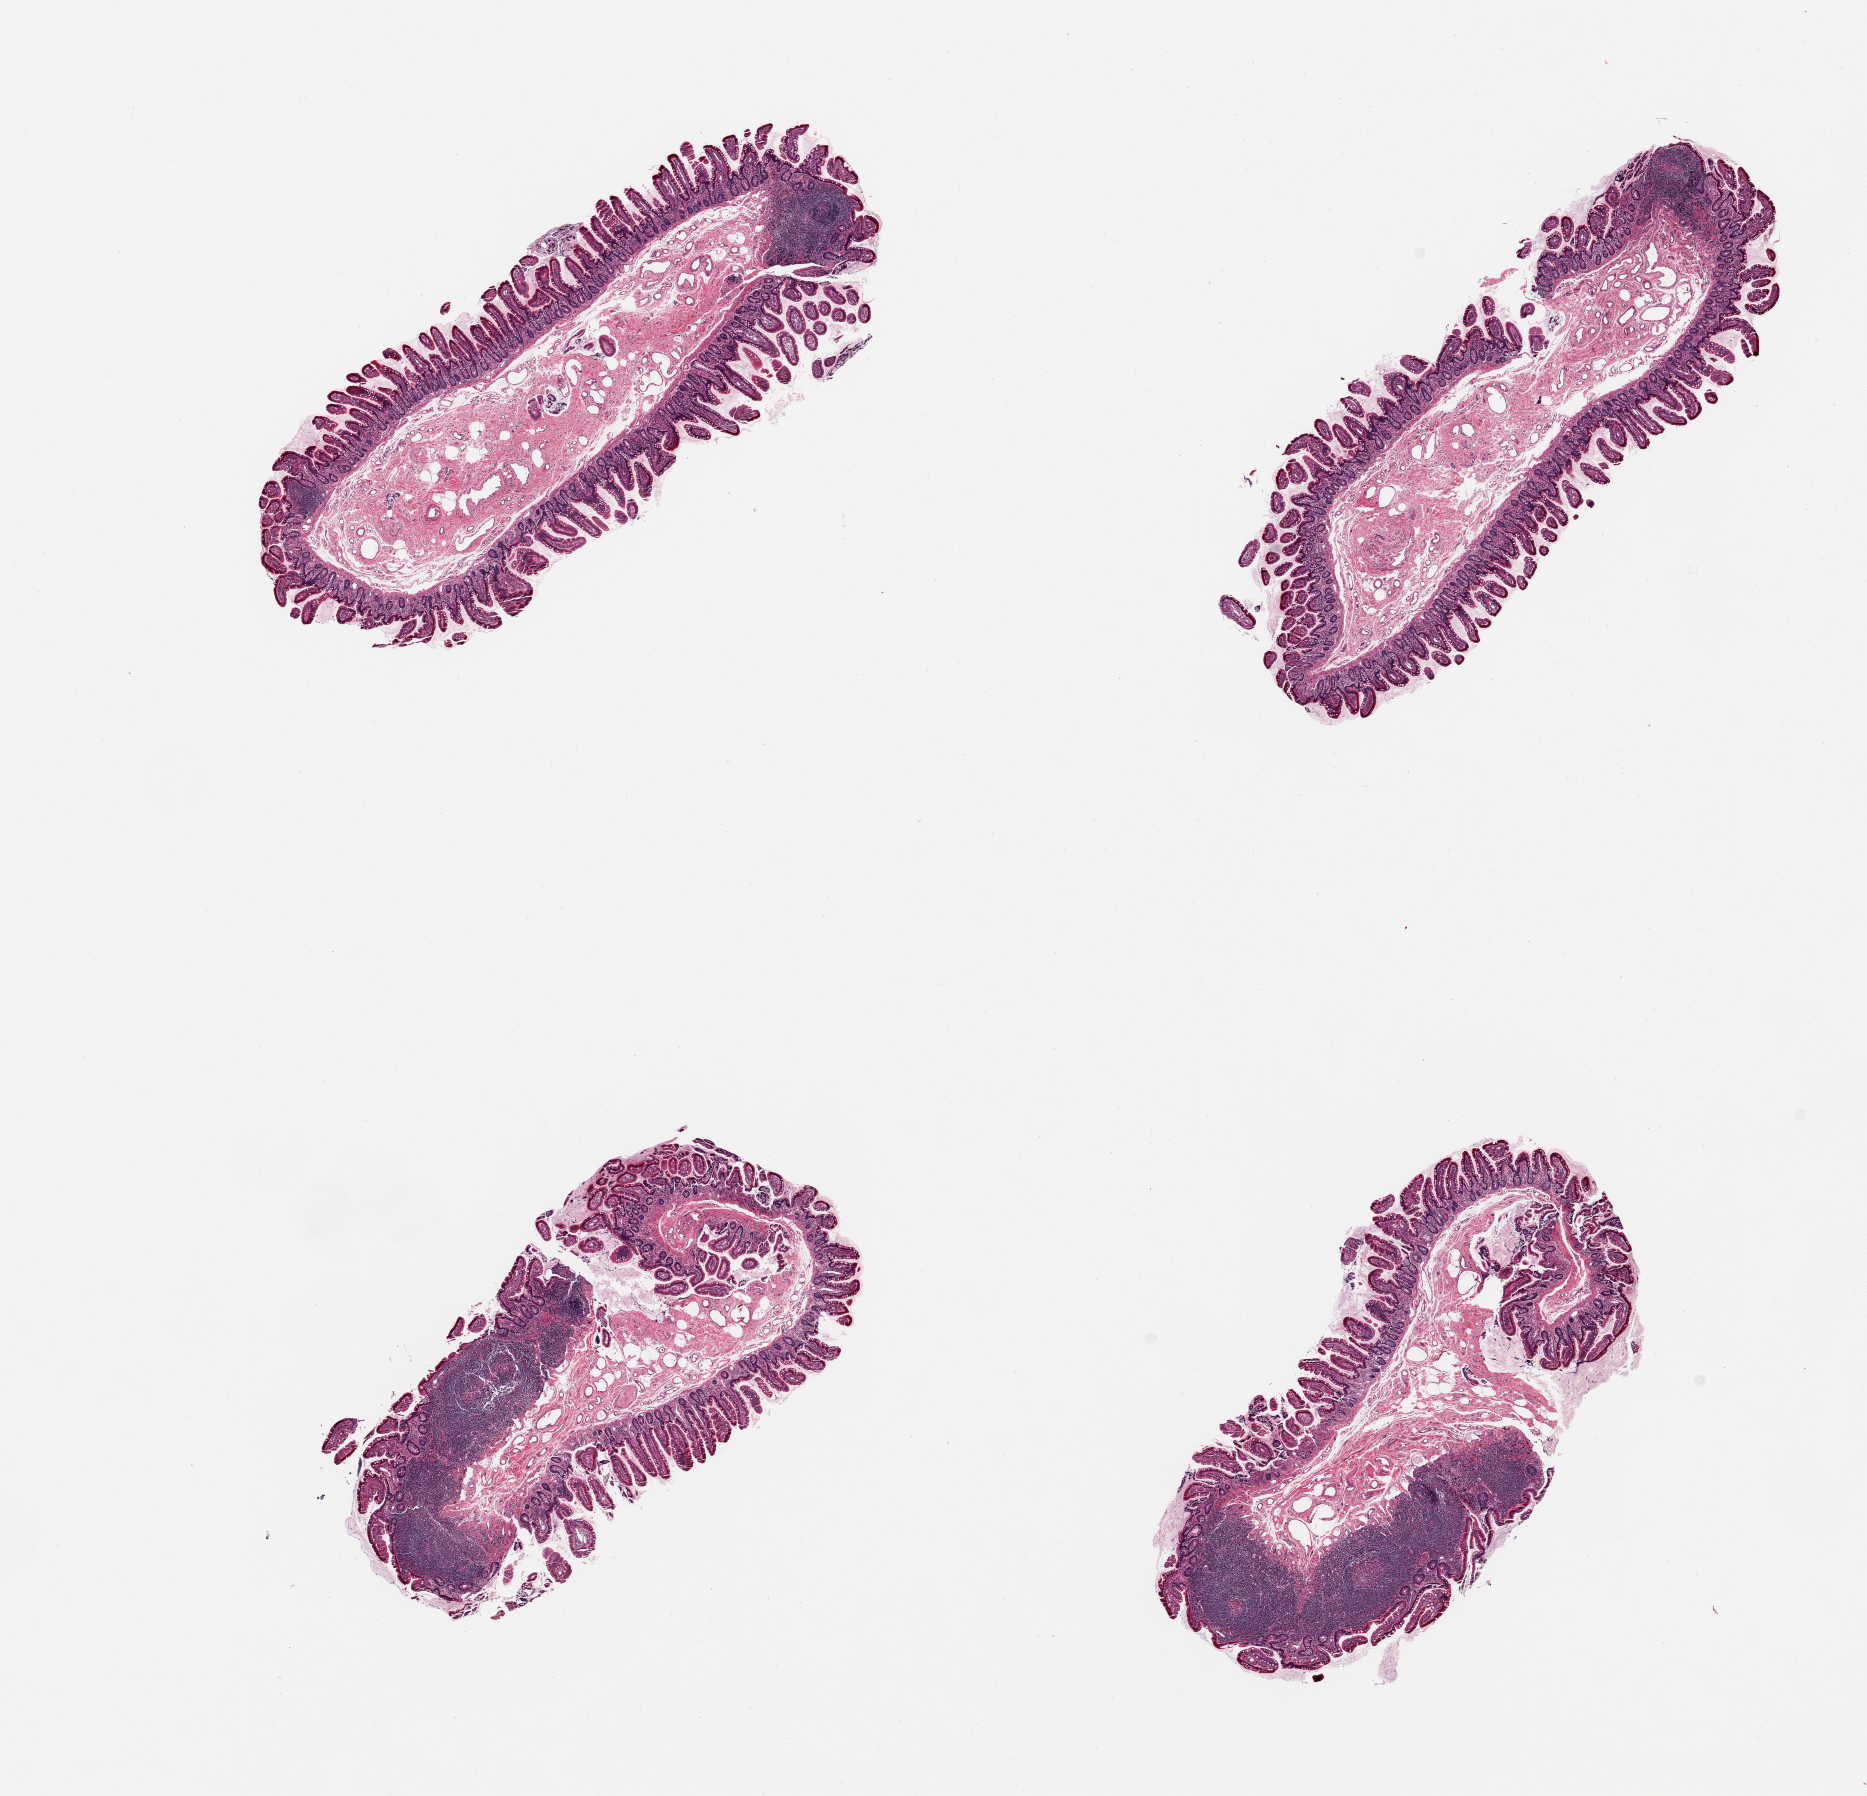
Digitized H&E-stained section, brightfield — shown as a low-resolution overview of the whole scanned area (about 14.8 x 14.2 mm). PAXgene-fixed paraffin-embedded (PFPE) section. Section of ileum (target tissue). Donor tissue sample. Donor sex: female.
* pathologist's review note for this sample: 4 pieces, well p`reserved mucoa; lymphoid aggregates are ~20% specimen